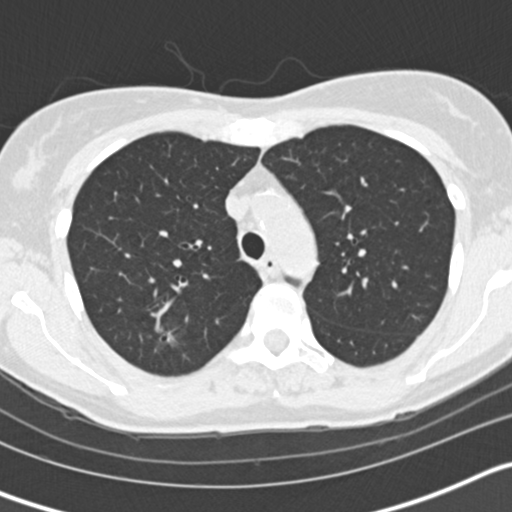
Chest CT (low-dose screening protocol), one axial image; second screening round (one year after baseline); lung window (W 1500 / L -600 HU); 2 mm slice thickness; standard (soft-tissue) reconstruction kernel (B30f). Female, age 58 years at enrolment.
Expert reader's lesion annotation, bounding box <138,317,197,367> (left, top, right, bottom; pixels). The screening reader recorded 3 non-calcified nodules or masses ≥4 mm on this exam (right upper lobe, left upper lobe, left lower lobe); which of them this box marks is not recorded. Participant outcome: lung cancer diagnosed 59 days after this screen — bronchiolo-alveolar adenocarcinoma, NOS, right upper lobe, moderately differentiated (G2), stage IA (AJCC 6th edition), 7 mm at pathology.